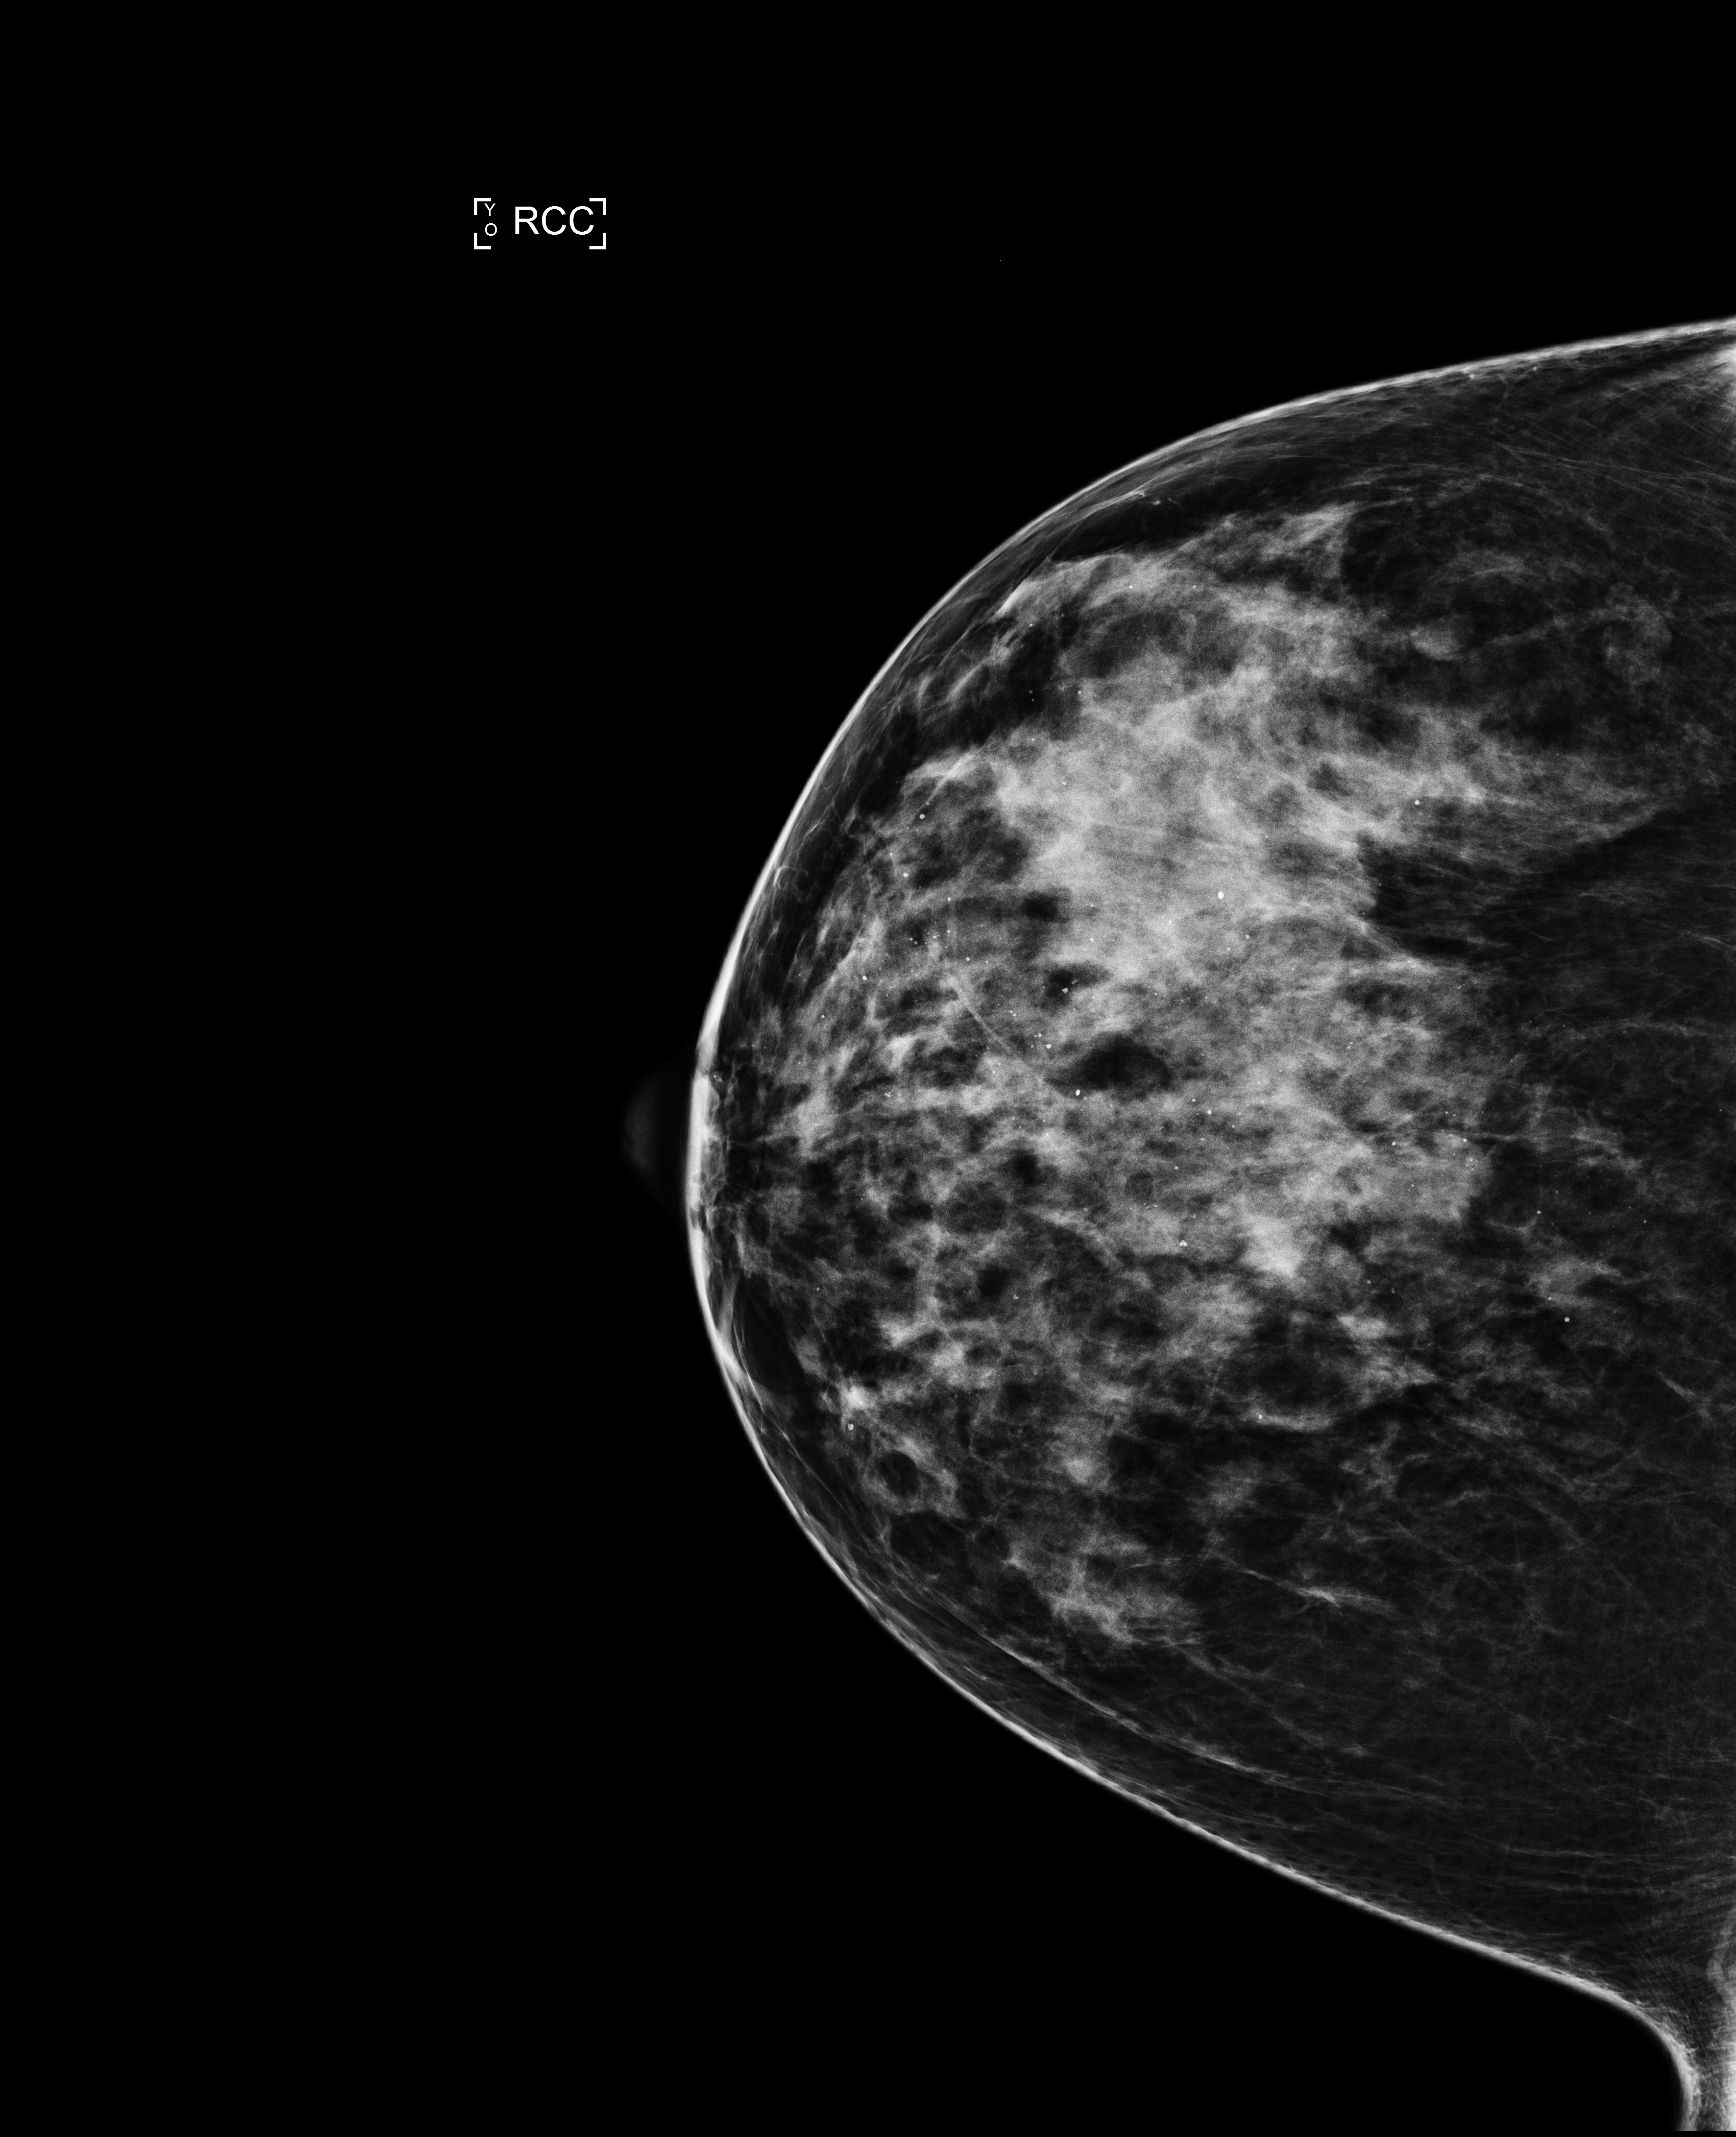
Annual screening mammography examination. Patient aged 46 years (female).
Image type: full-field digital mammogram. Breast: right. Projection: cranio-caudal projection.